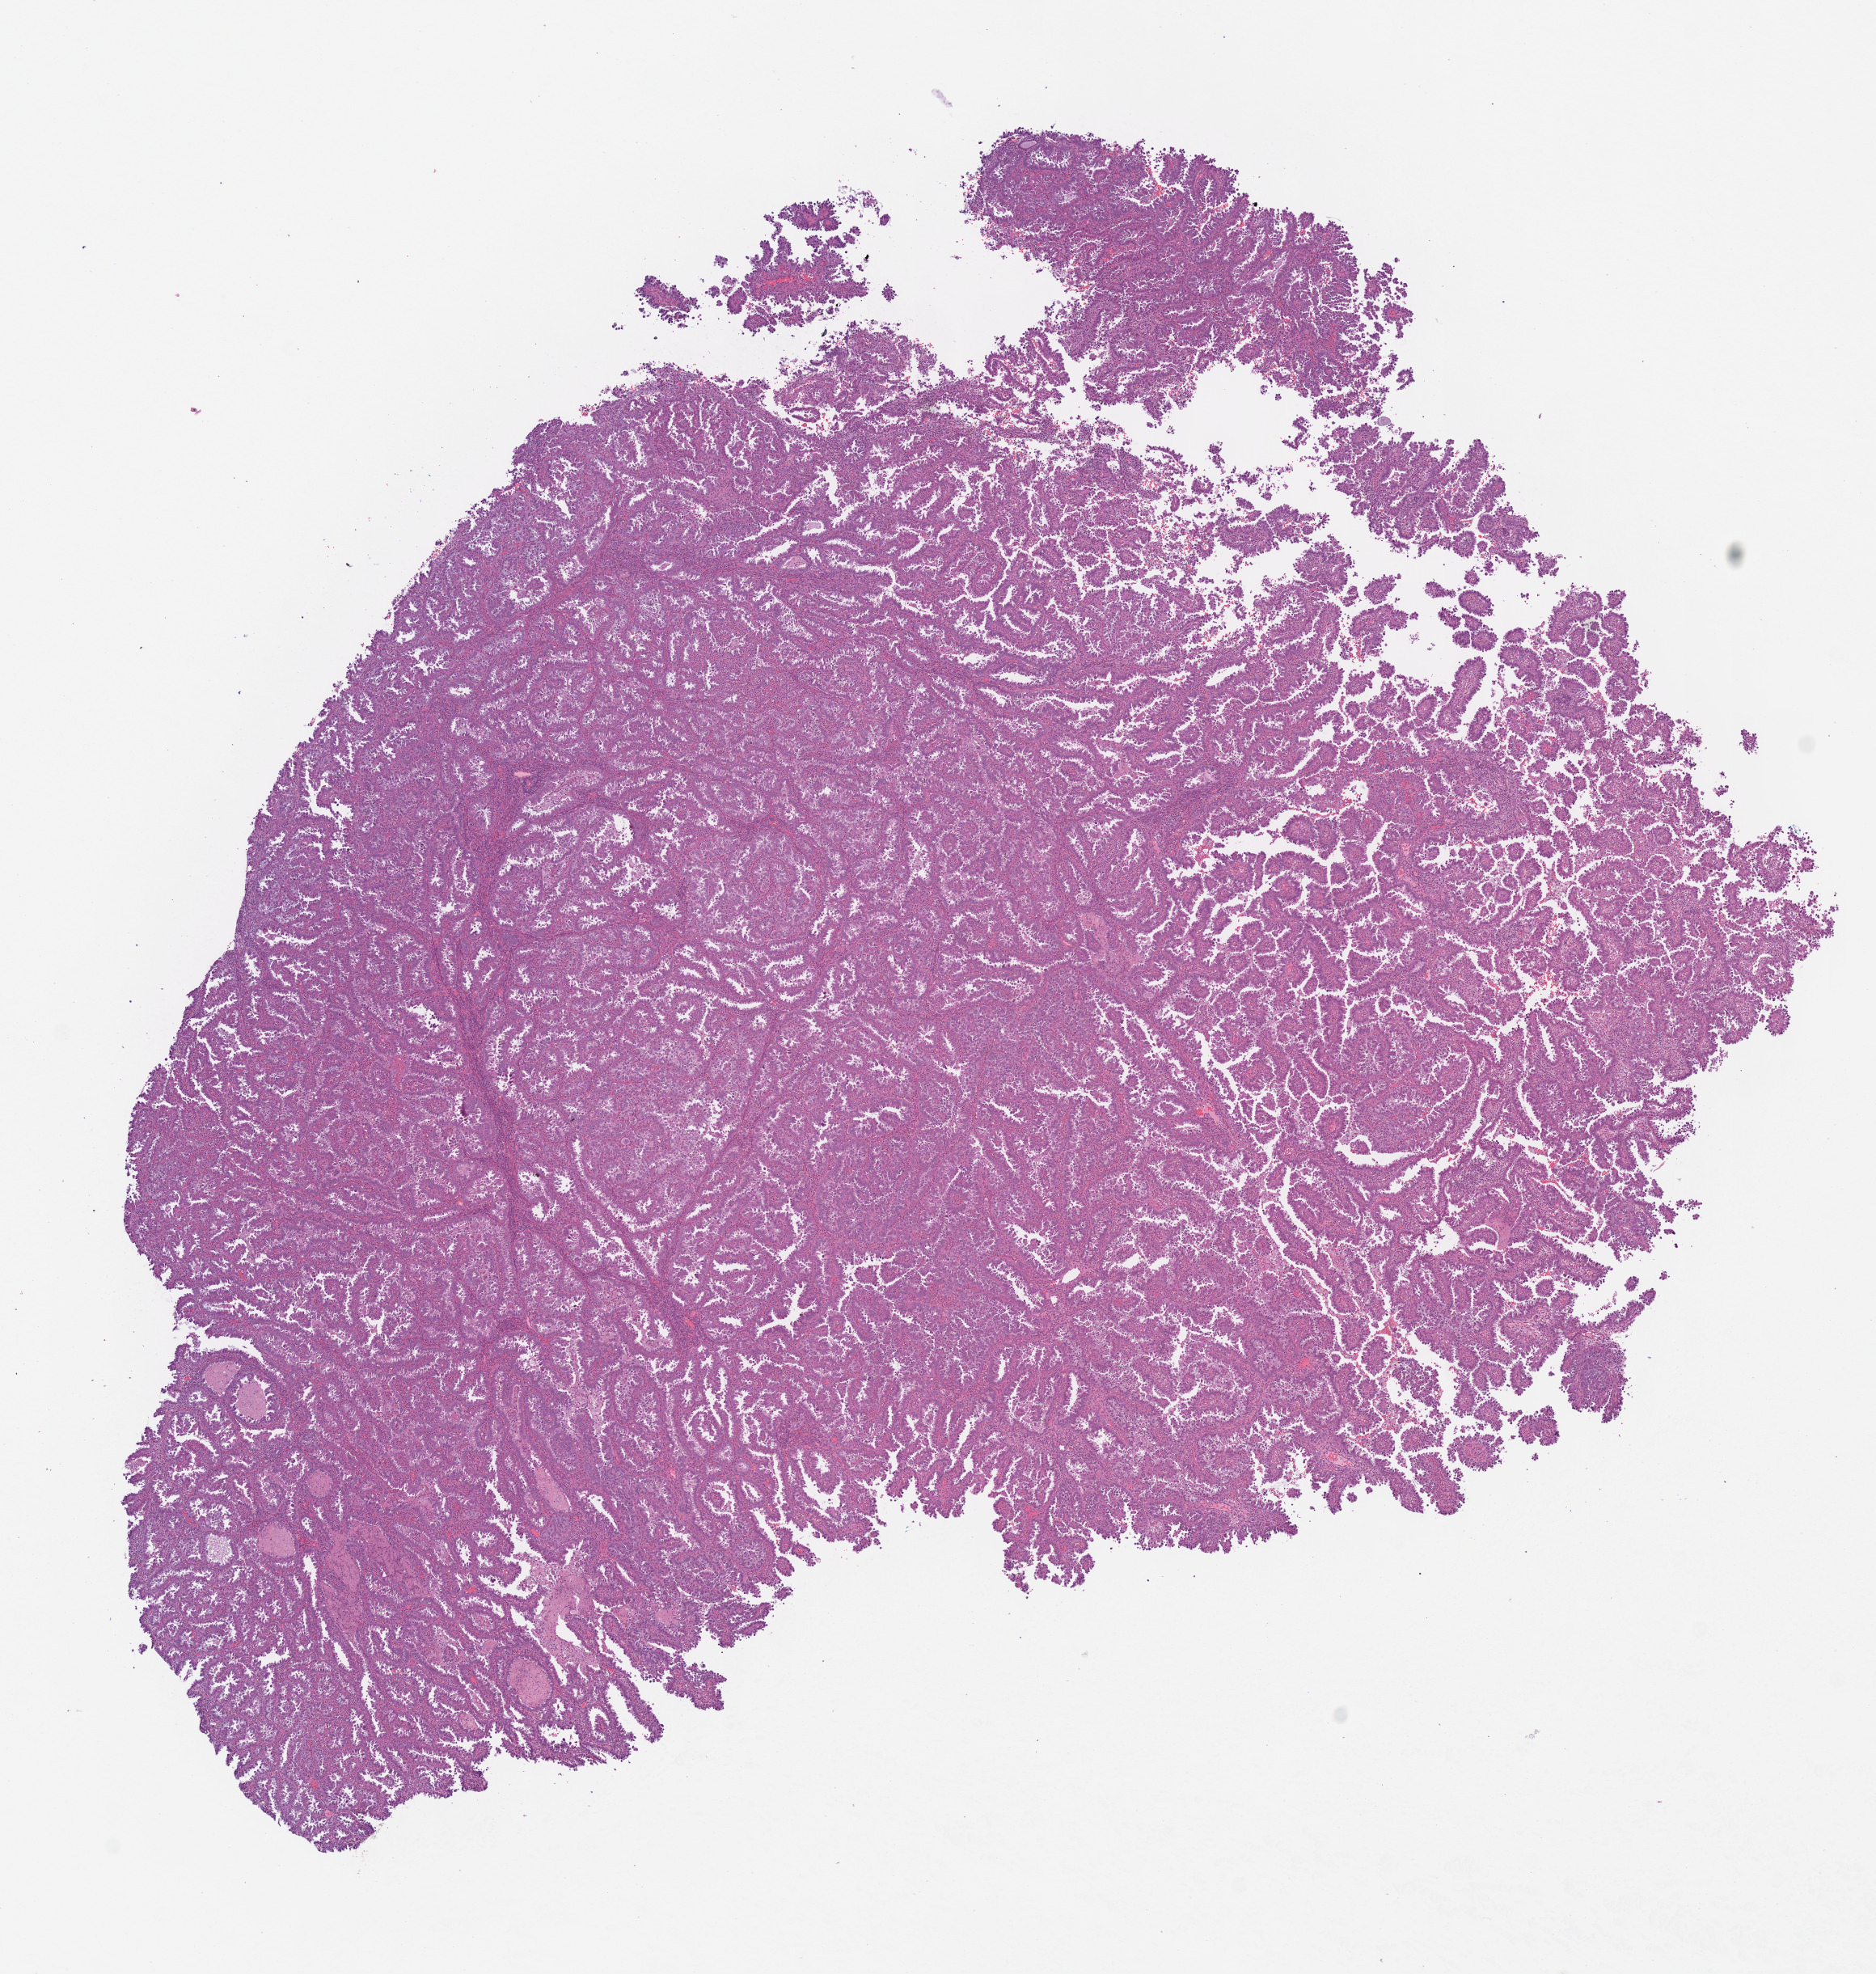
H&E whole-slide image — whole scanned area (about 9.1 x 9.6 mm) shown as a low-resolution overview; formalin-fixed paraffin-embedded (FFPE) diagnostic section; sample: primary tumour, uterus. Female patient; age at initial diagnosis 67 years. Histologic grade: G3 (poorly differentiated).
Pathologic diagnosis: Serous cystadenocarcinoma, NOS (endometrium). FIGO stage: II.